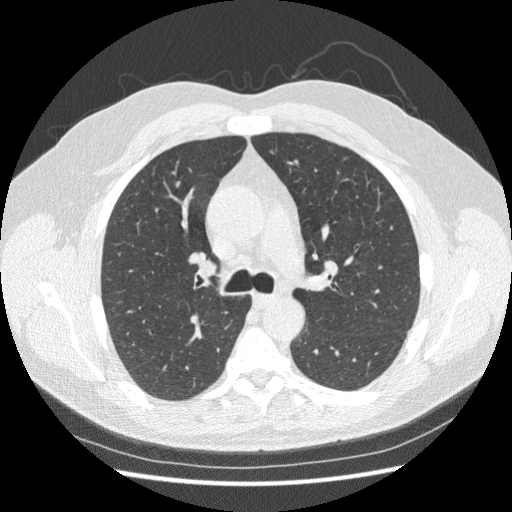
Low-dose screening chest CT, one axial slice. Slice 157 of 250 in the series (ordered by position). Reconstruction kernel STANDARD. 120 kVp. Lung window (W 1500 / L -600 HU). 1.25 mm slice thickness. 512 × 512 image matrix, field of view 360 × 360 mm.
Annotated regions visible in this slice (outlined manually by an expert reader):
- lesion 1 (tumor, upper lobe of right lung): bounding box (x1, y1, x2, y2) in pixels: (176, 180, 181, 188)